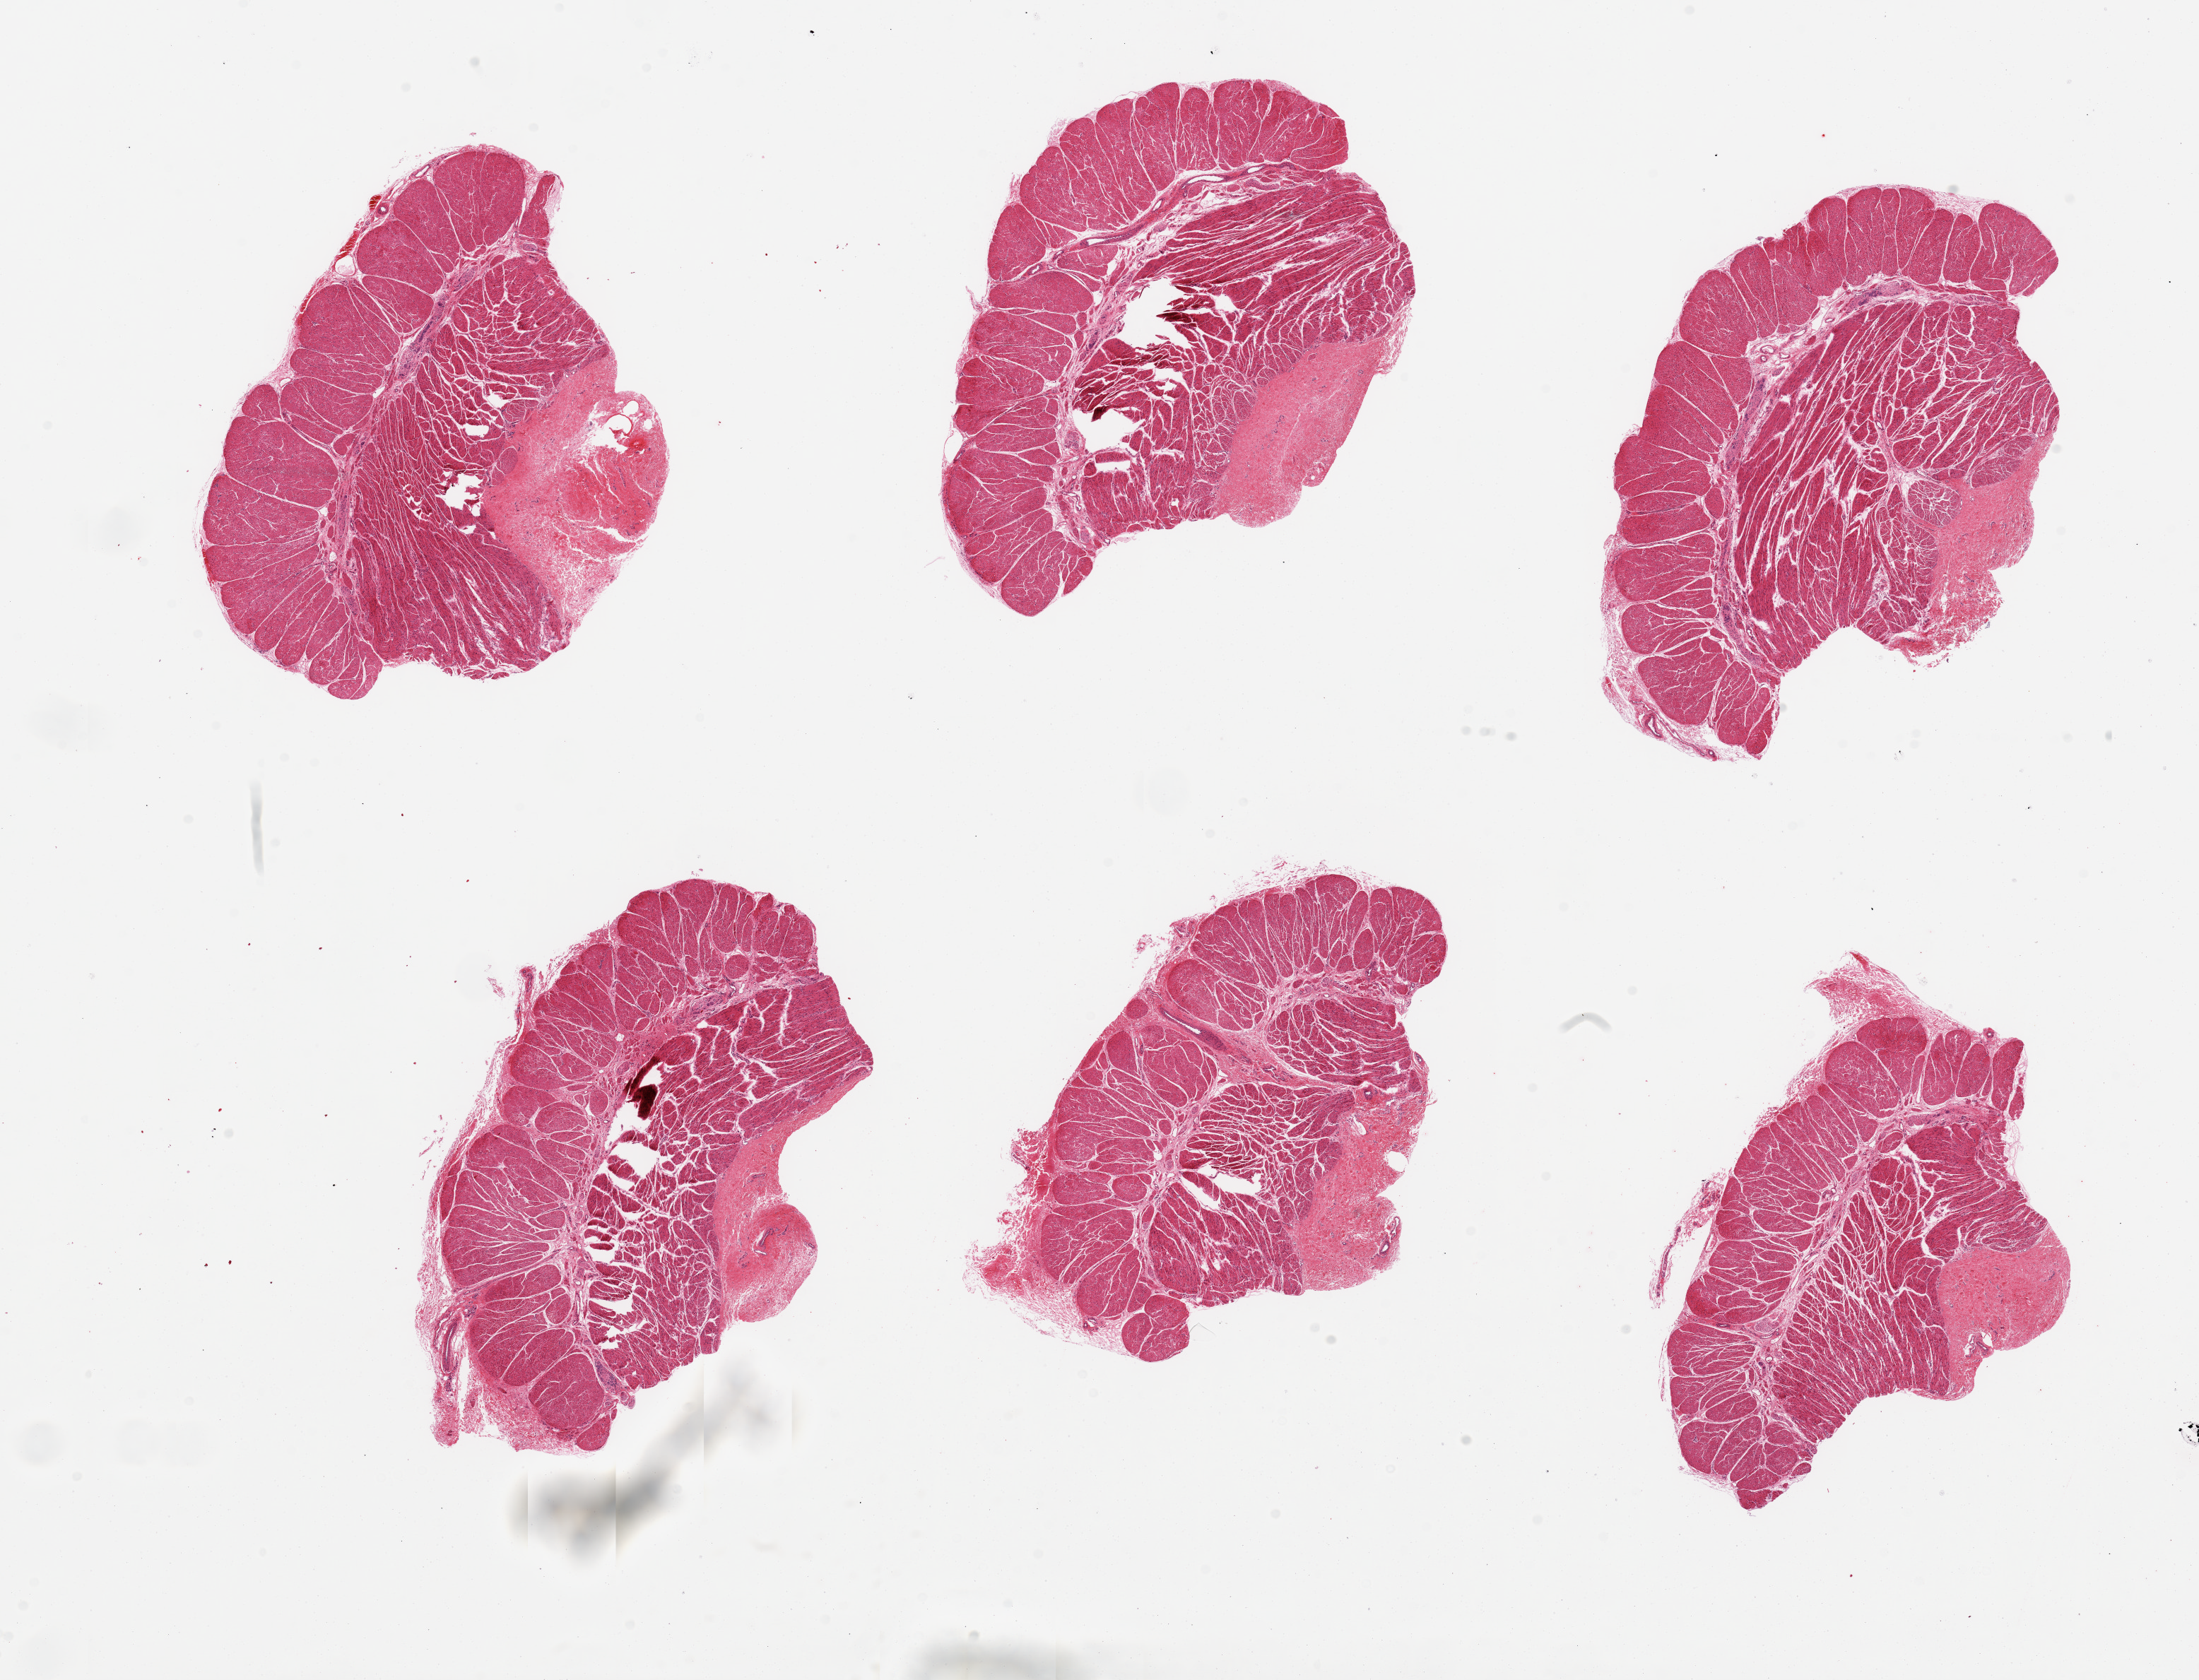
Hematoxylin and eosin (H&E) whole-slide image — shown as a low-resolution overview of the whole scanned area (about 24.6 x 18.8 mm, acquisition: 20x scan); PAXgene-fixed paraffin-embedded (PFPE) section; target tissue: esophageal muscle; tissue donor sample. Donor sex: female.
• pathologist's review note for this sample: 6 pieces, well trimmed